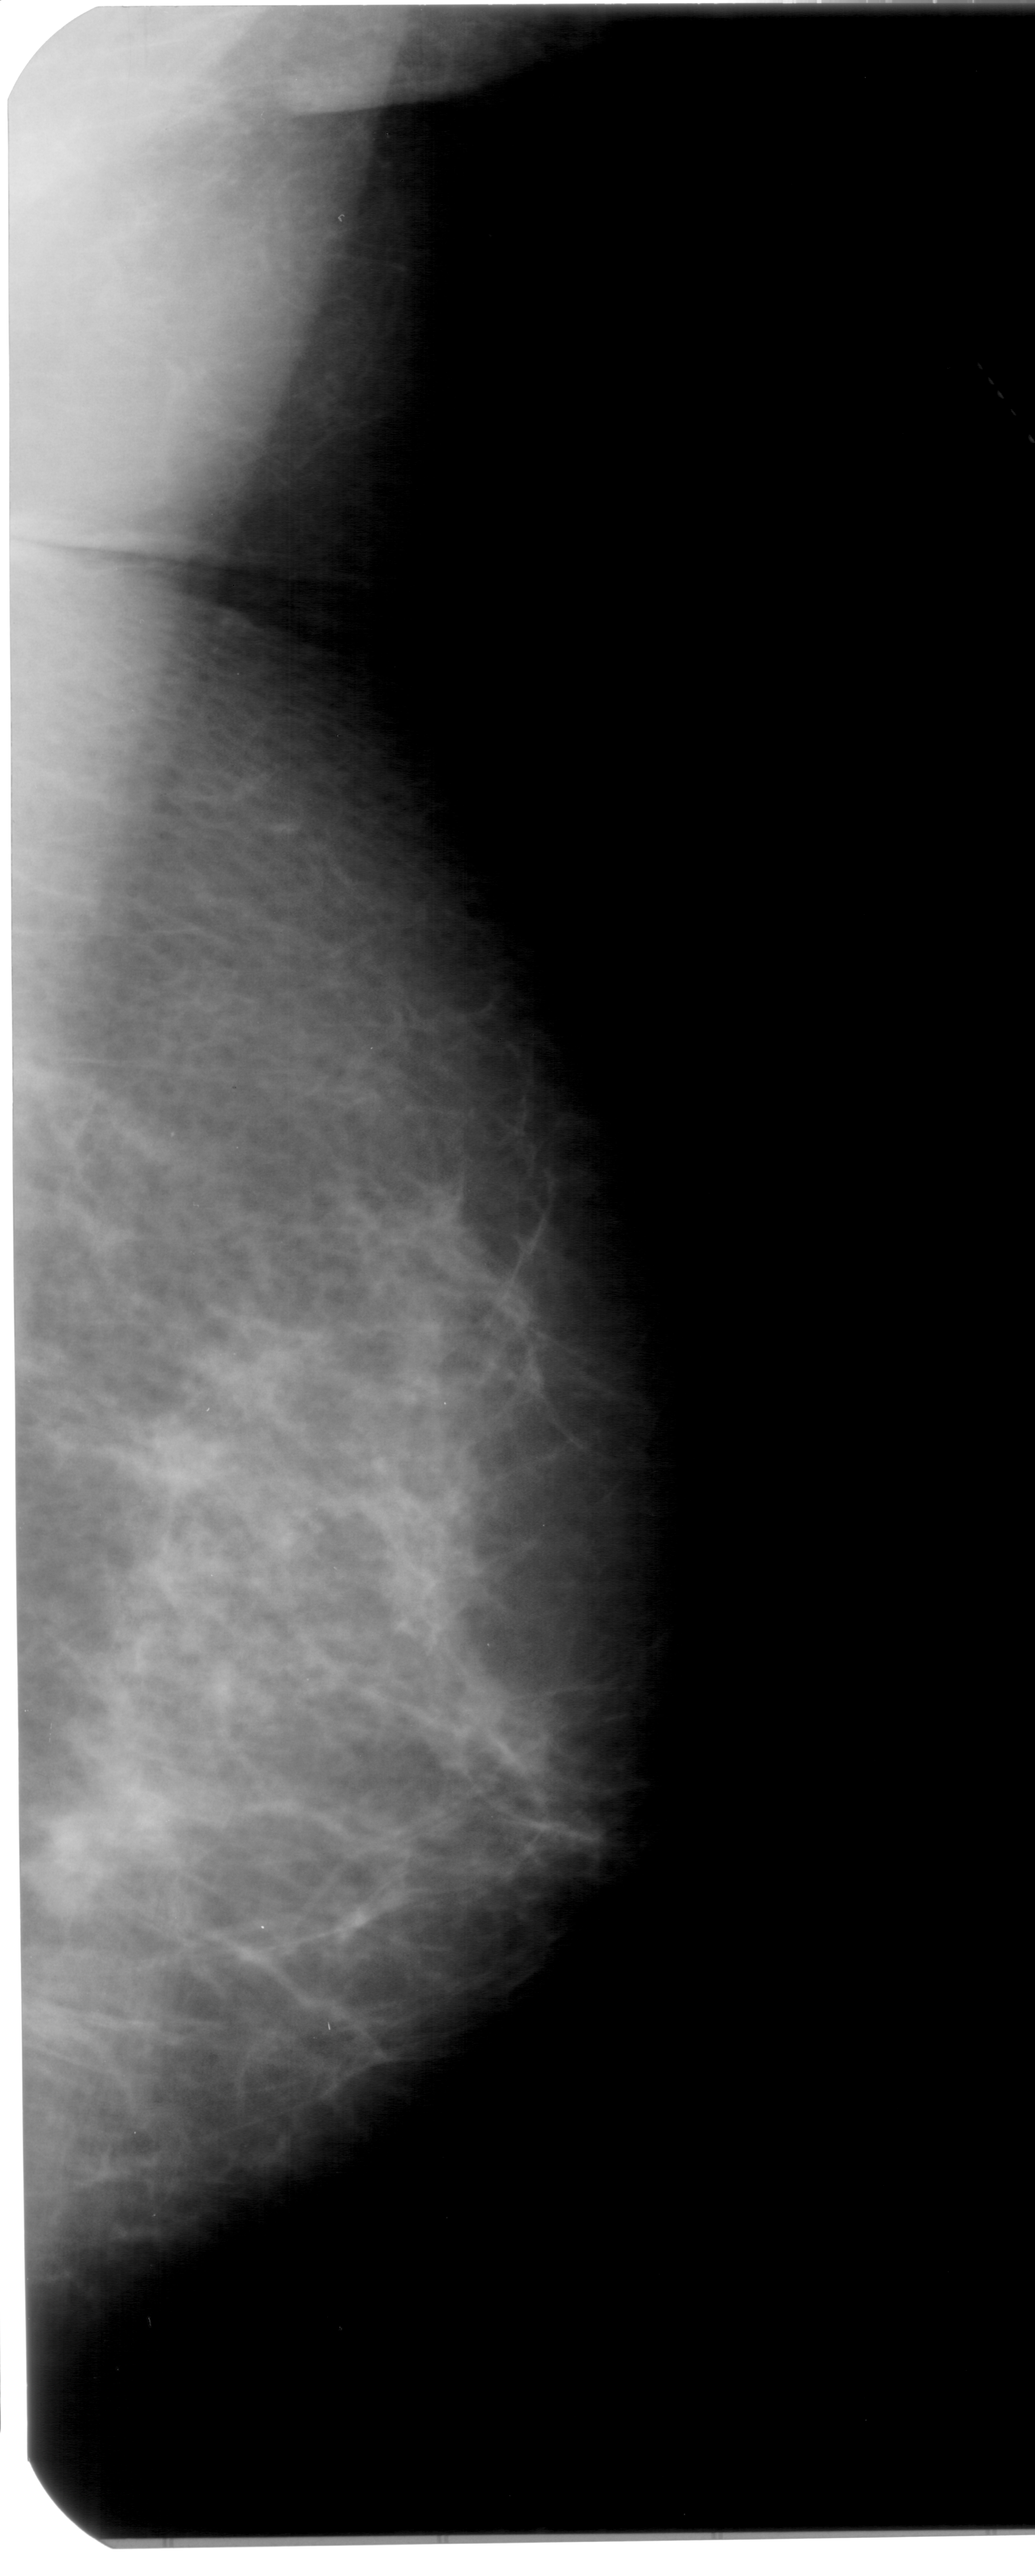
Mammogram (digitized film); right breast; MLO view; BI-RADS breast density category 2 (scale 1–4).
Radiologist-marked abnormalities on this image: mass, shape focal asymmetric density, margins ill defined; BI-RADS assessment category 4; pathology (as recorded): benign.